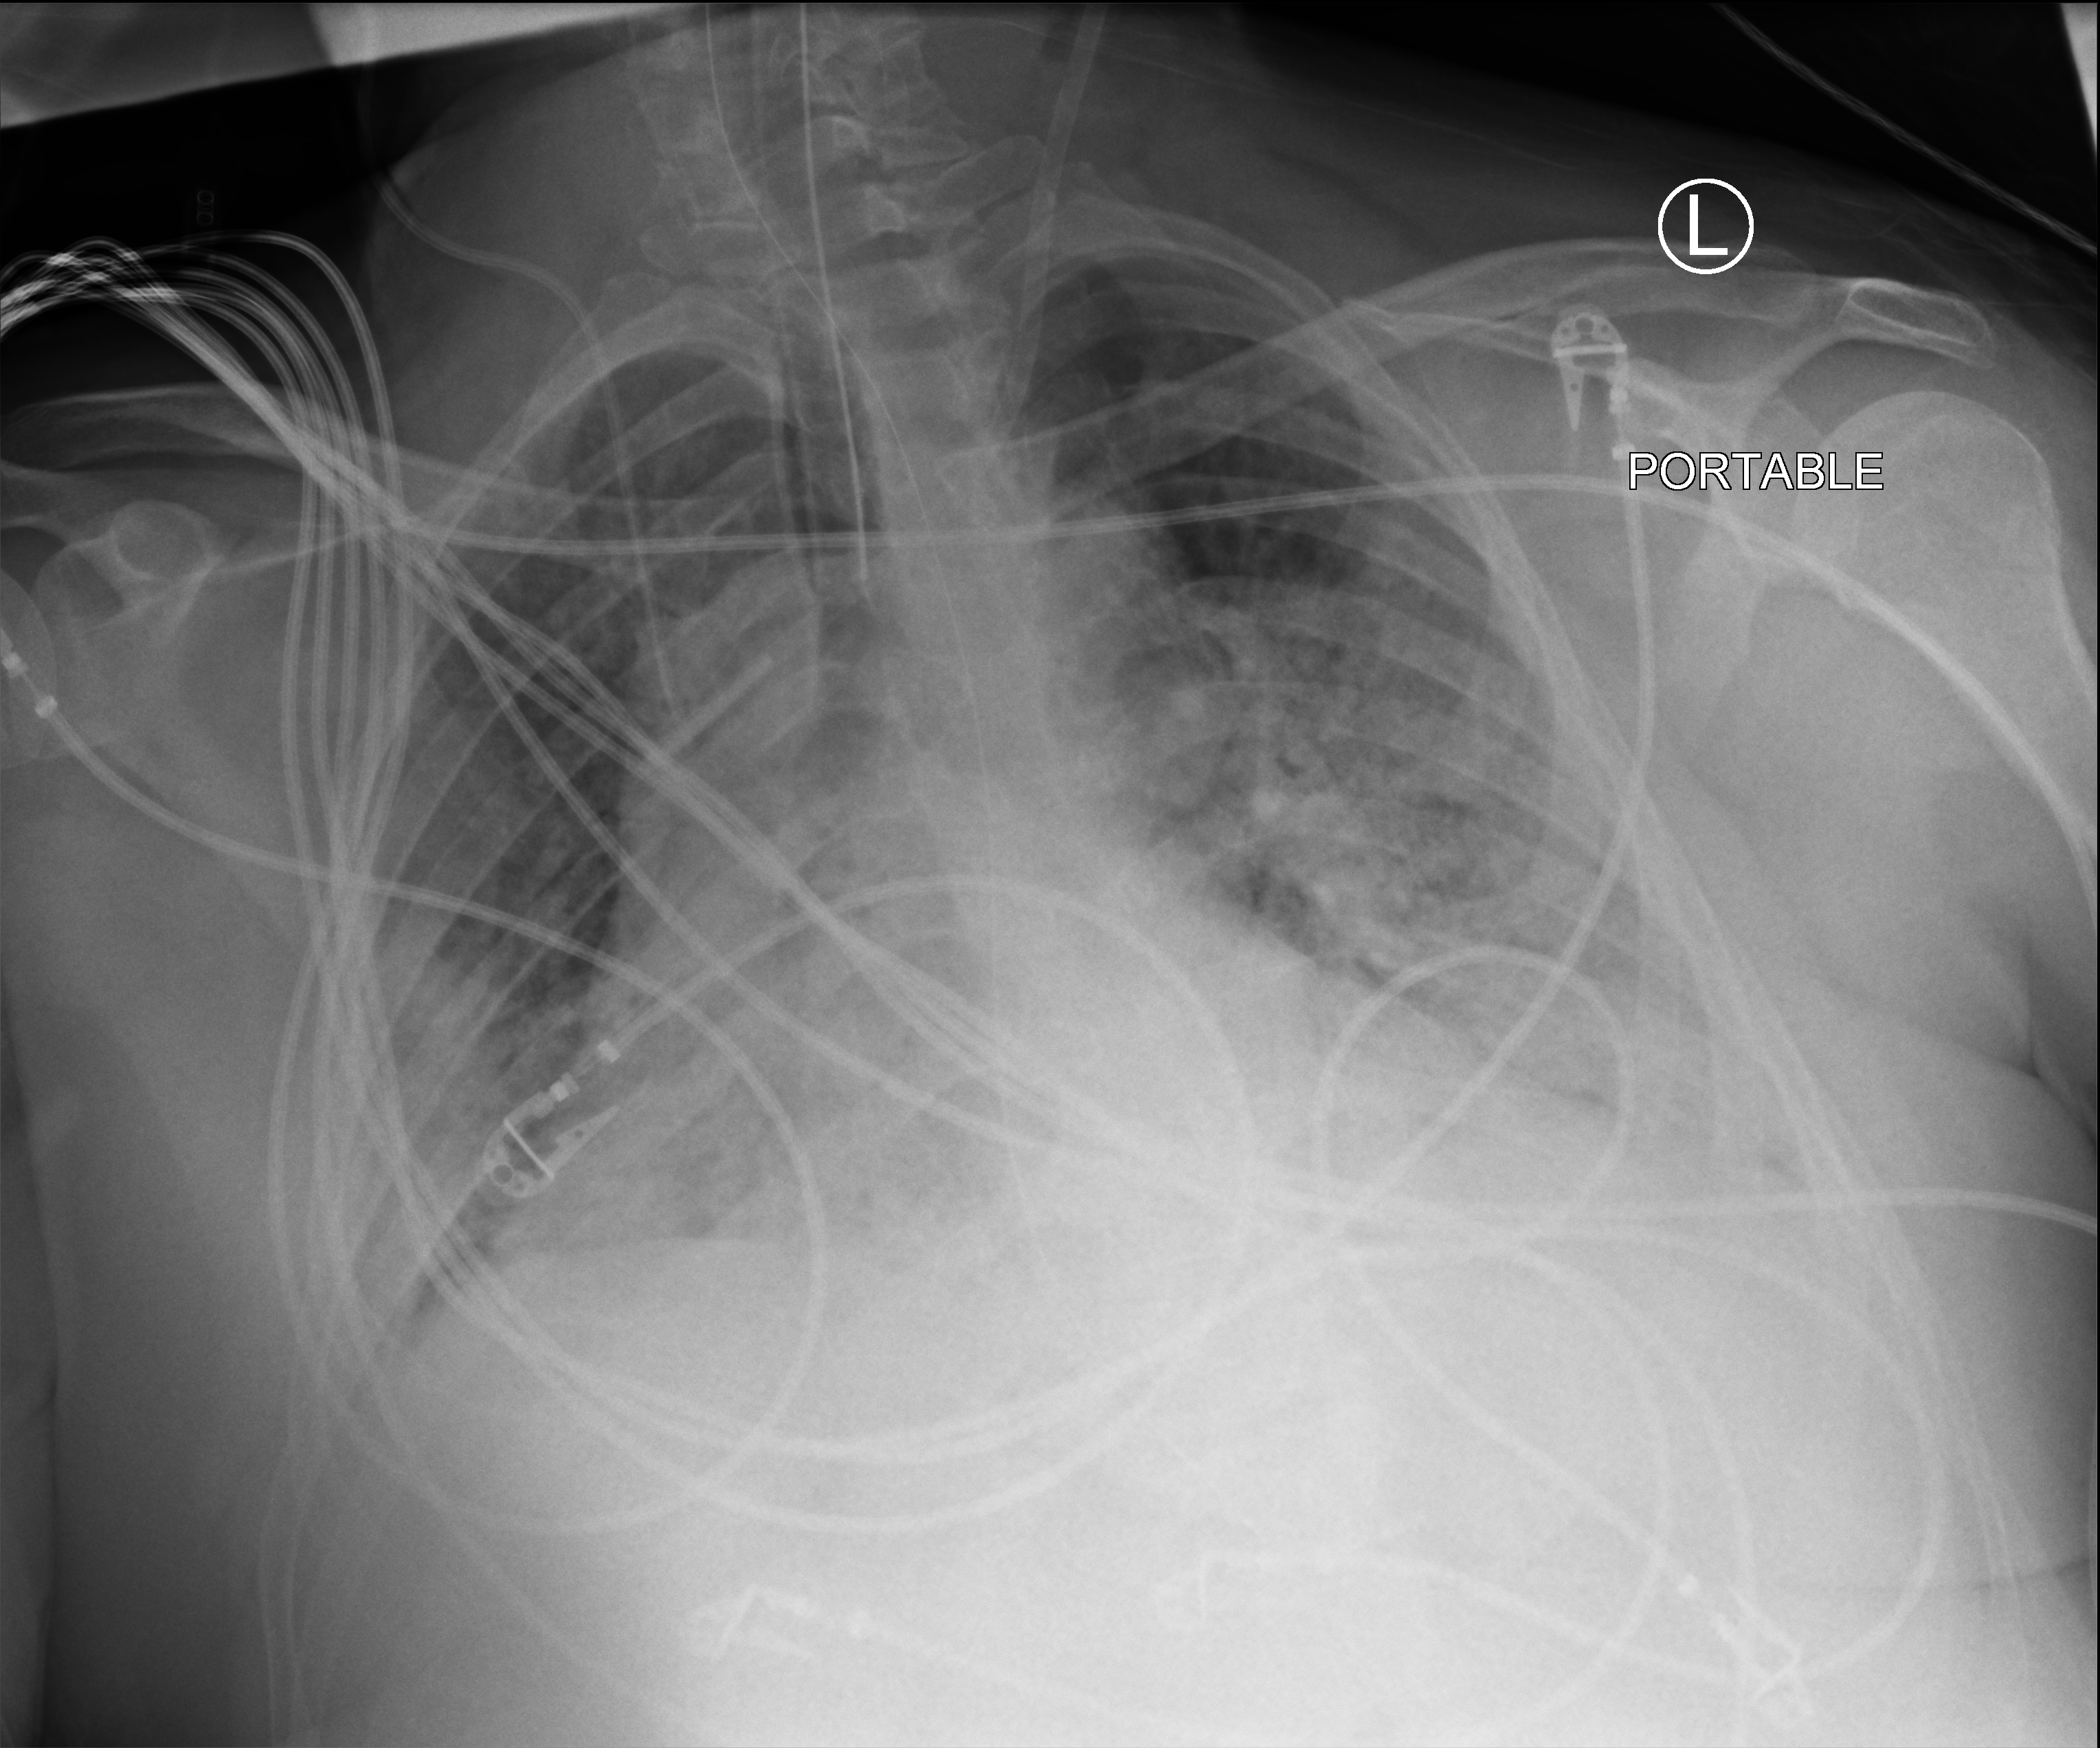
Bedside chest radiograph (computed radiography); anteroposterior (AP) projection. Patient hospitalised with COVID-19; male, aged 18–59 years.
Admission-level facts for this patient (not findings on this image; timing relative to this image not recorded):
- hypertension (admission record): yes
- smoking status (admission record): never
- admitted to intensive care during this hospital stay: yes